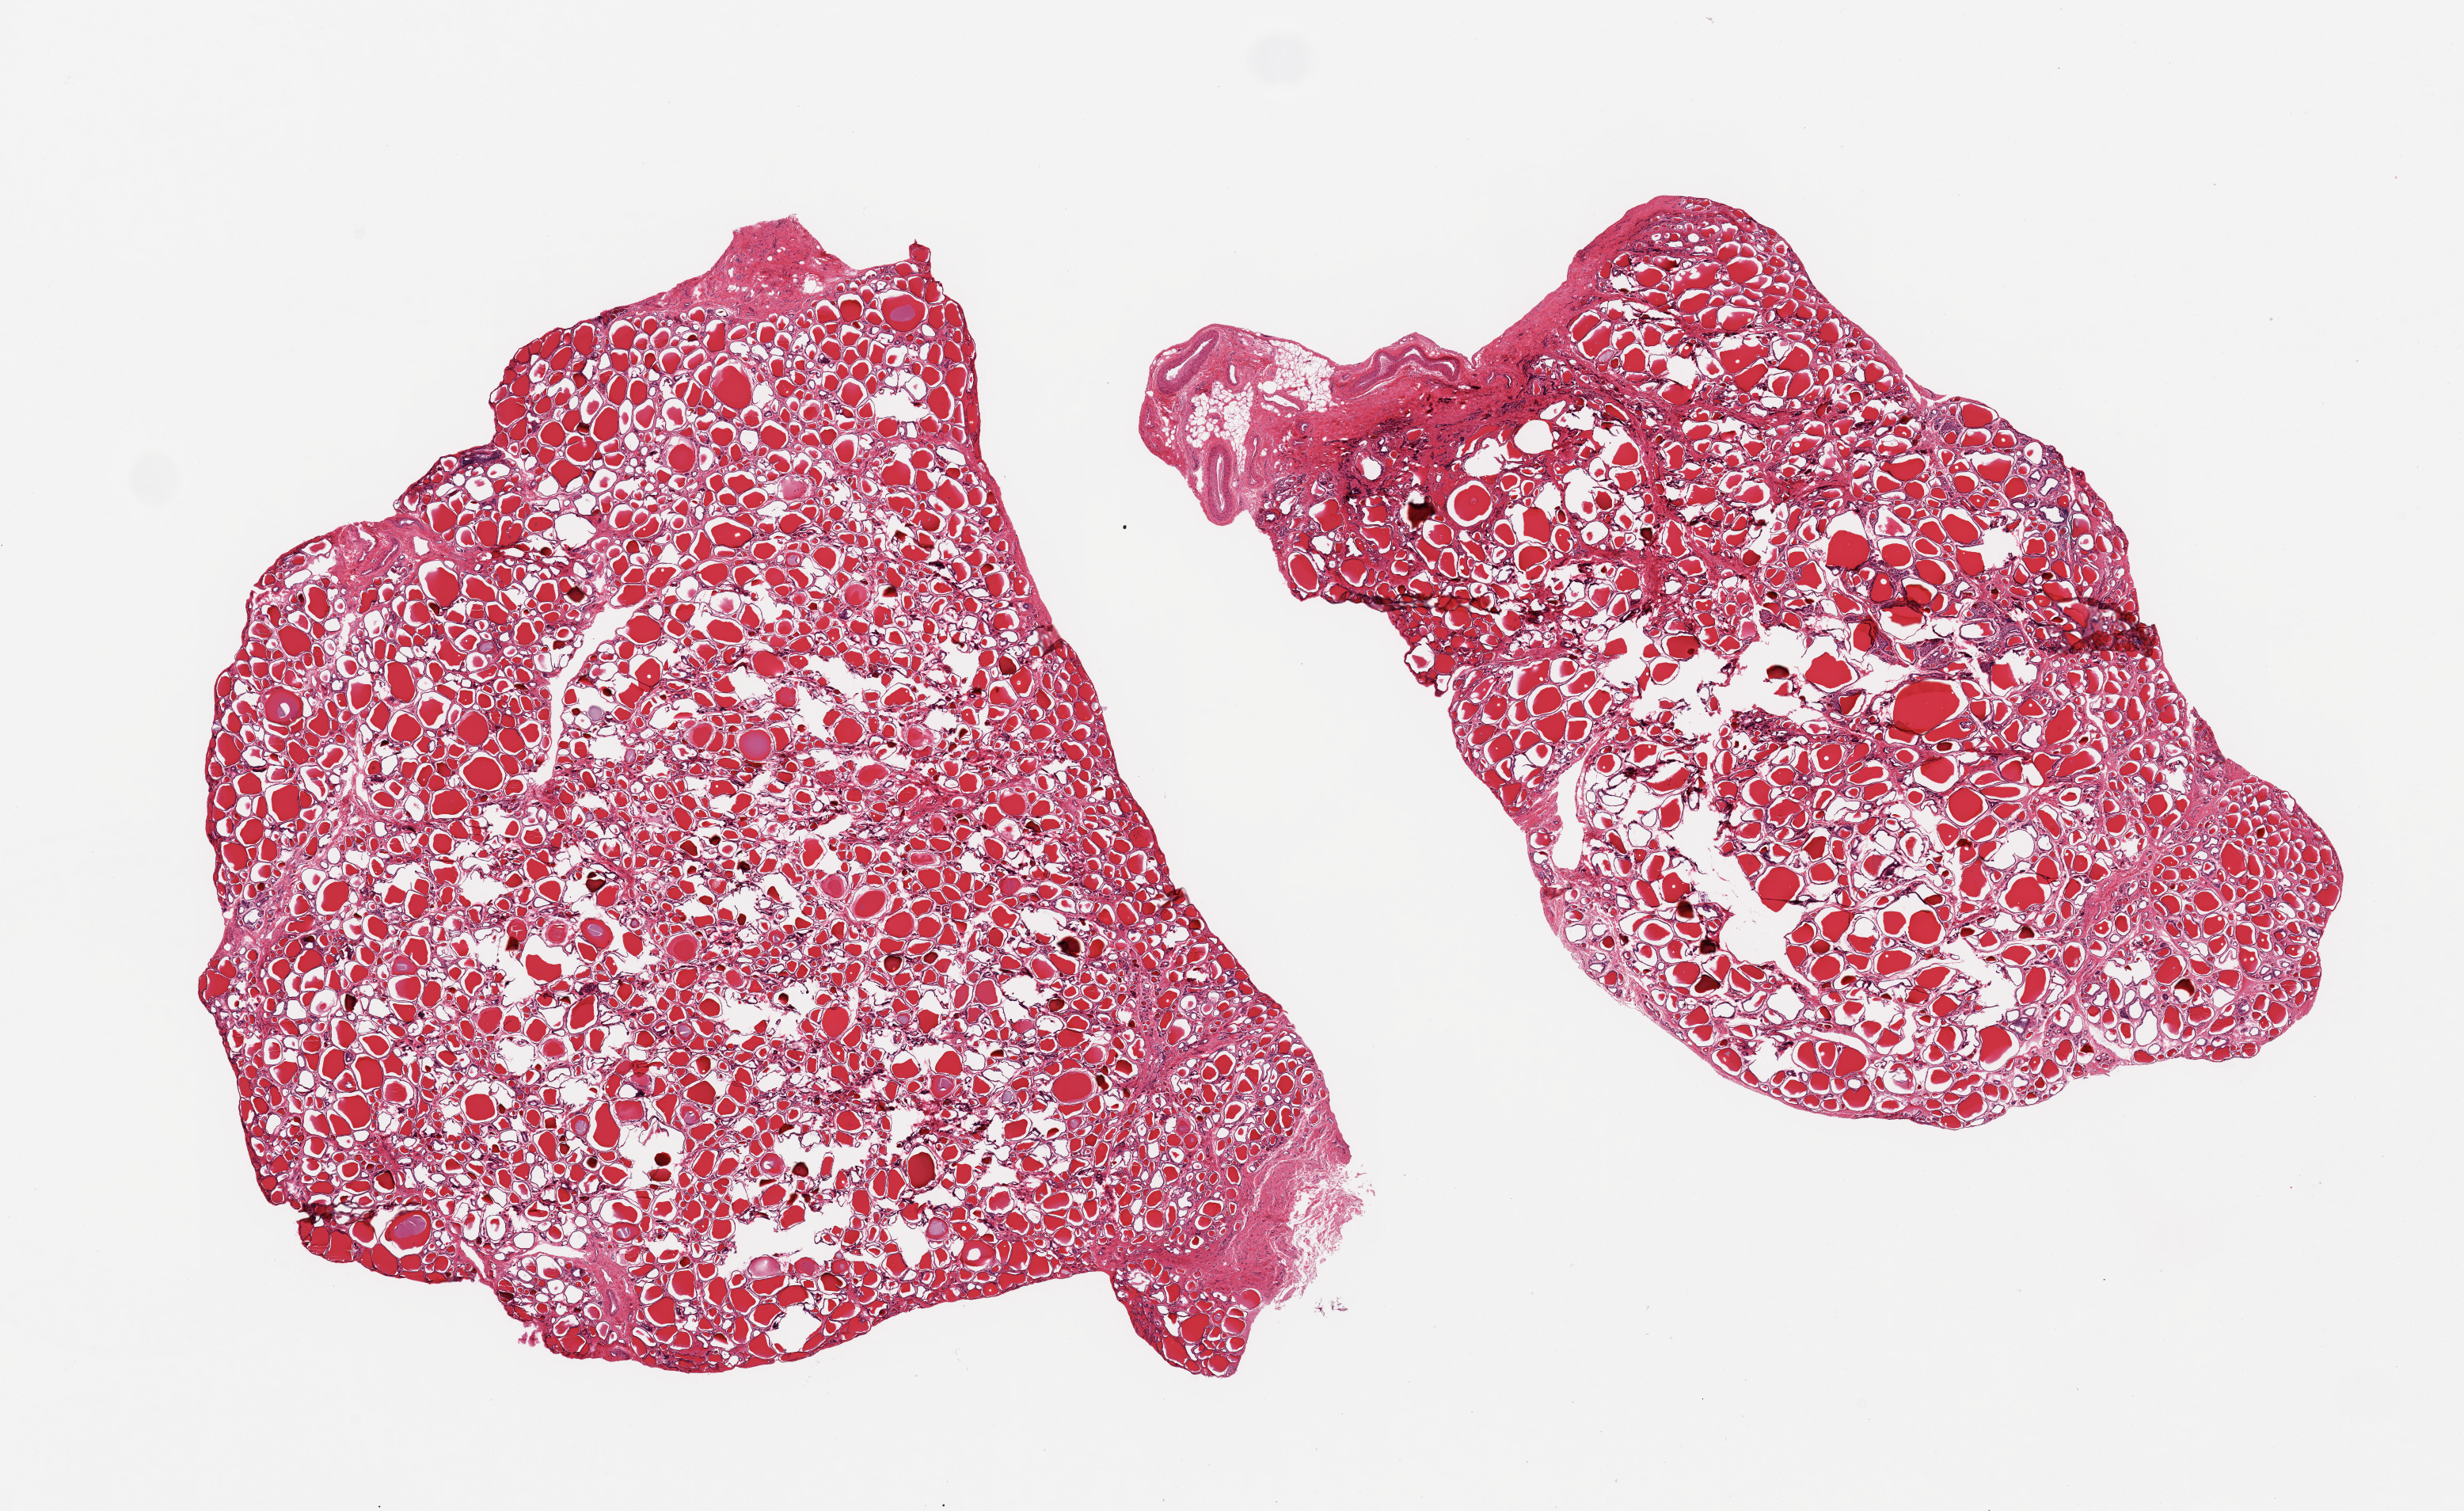
Whole-slide image, H&E stain, brightfield, shown as a low-resolution overview of the whole scanned area (about 24.6 x 15.1 mm, from a 20x scan), PAXgene-fixed, paraffin-embedded tissue, section of thyroid (target tissue), donor tissue sample.
* reviewer comment on this tissue sample: 2 pieces, ~11x7mm